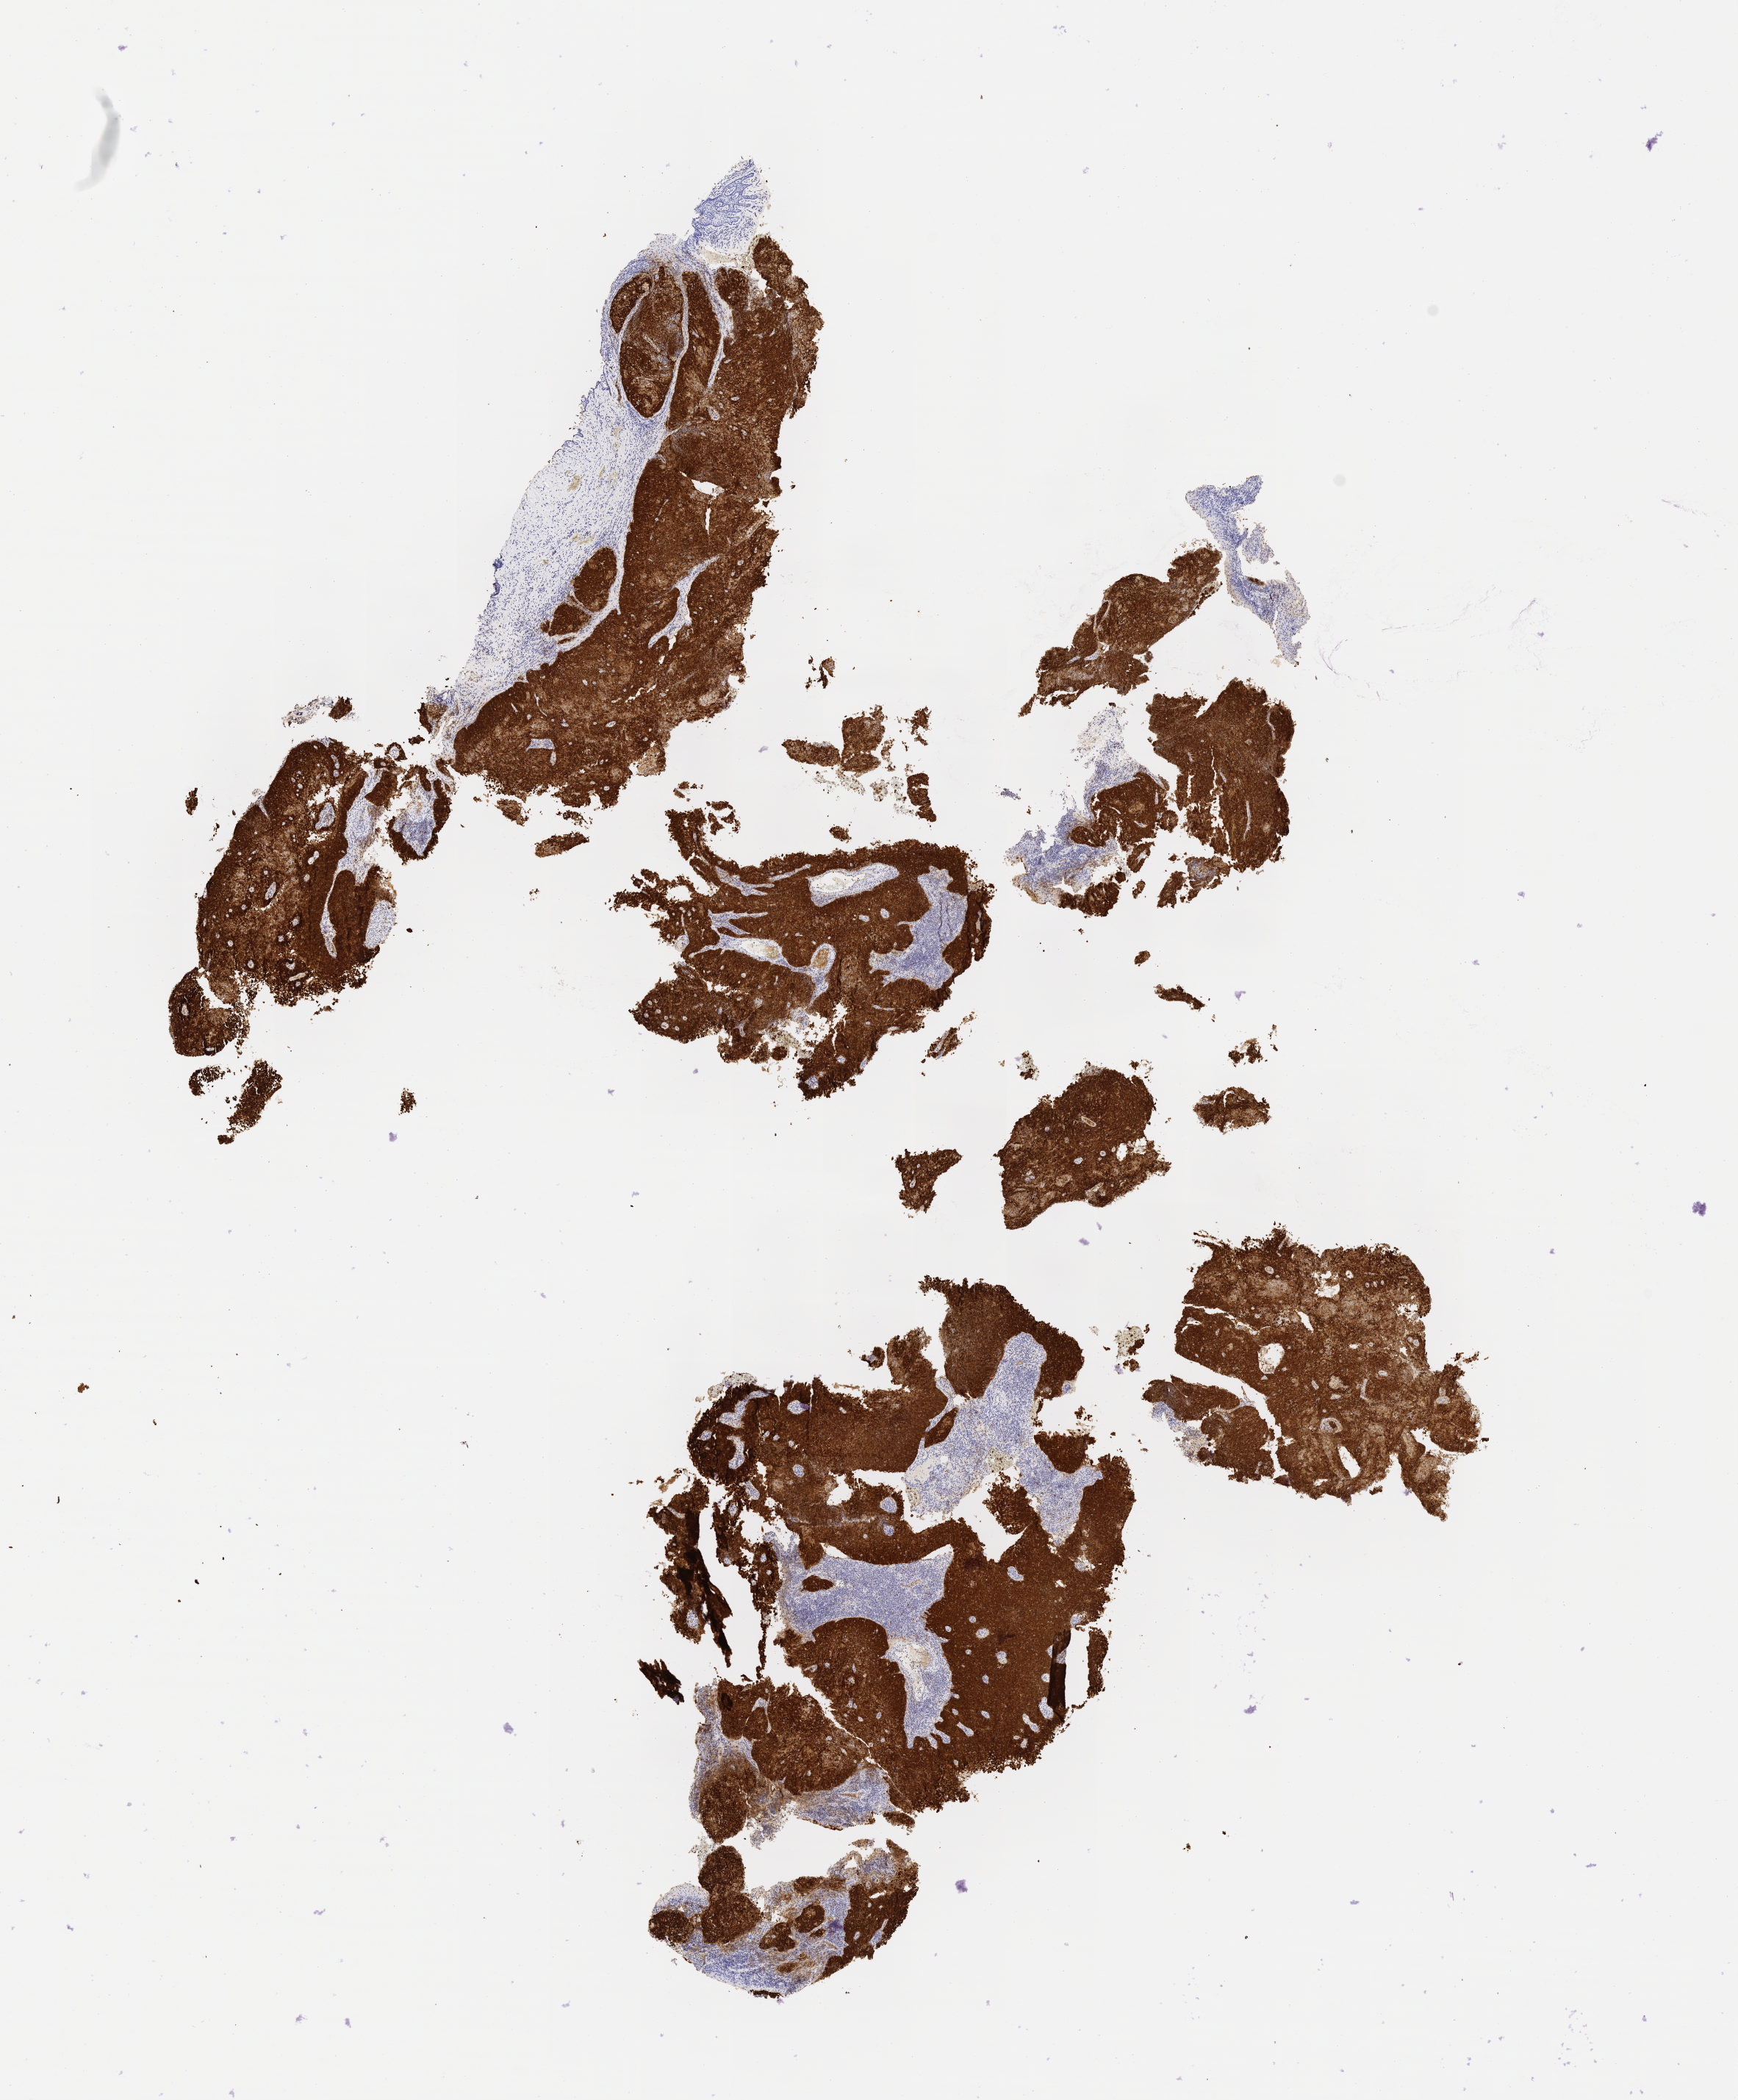
Immunohistochemistry (IHC) whole-slide image stained for p16 (p16INK4a) — low-resolution overview of the scanned area, about 9.6 x 11.5 mm, tumor tissue, anatomic site: cervix. Patient female; aged 40.
- histologic diagnosis: Squamous cell carcinoma, large cell, nonkeratinizing, NOS